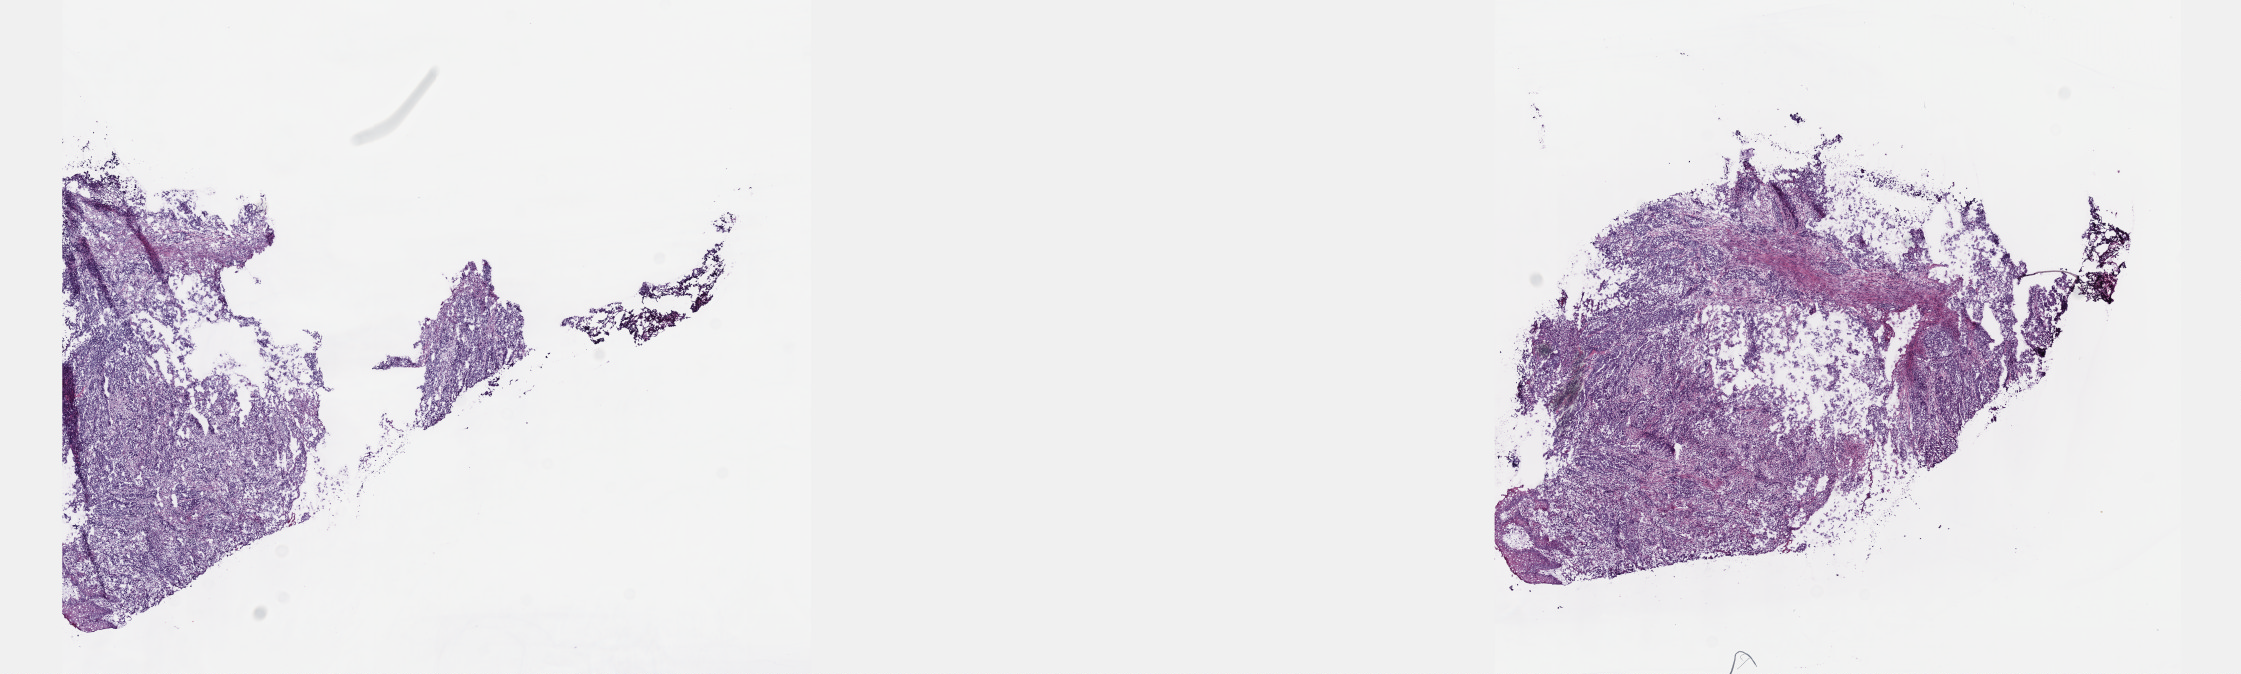
Whole-slide histology image, H&E, a low-resolution overview of the entire scanned area, about 18.1 x 5.4 mm, frozen section from the top of the tissue portion, esophagus, primary tumour sample. Male, age 79 years at initial diagnosis. Histologic grade: G3 (poorly differentiated). Pathologist review of this section (percent, as recorded): tumour cells 70%, tumour nuclei 100%, normal cells 0%, stromal cells 25%, necrosis 5%. Infiltration values recorded for this section: lymphocyte infiltration 4%, monocyte infiltration 4%, neutrophil infiltration 0%.
Lymph nodes positive (case pathology): 4 of 19 examined. Pathologic diagnosis: Adenocarcinoma, NOS (lower third of esophagus). AJCC pathologic stage: III (6th edition).